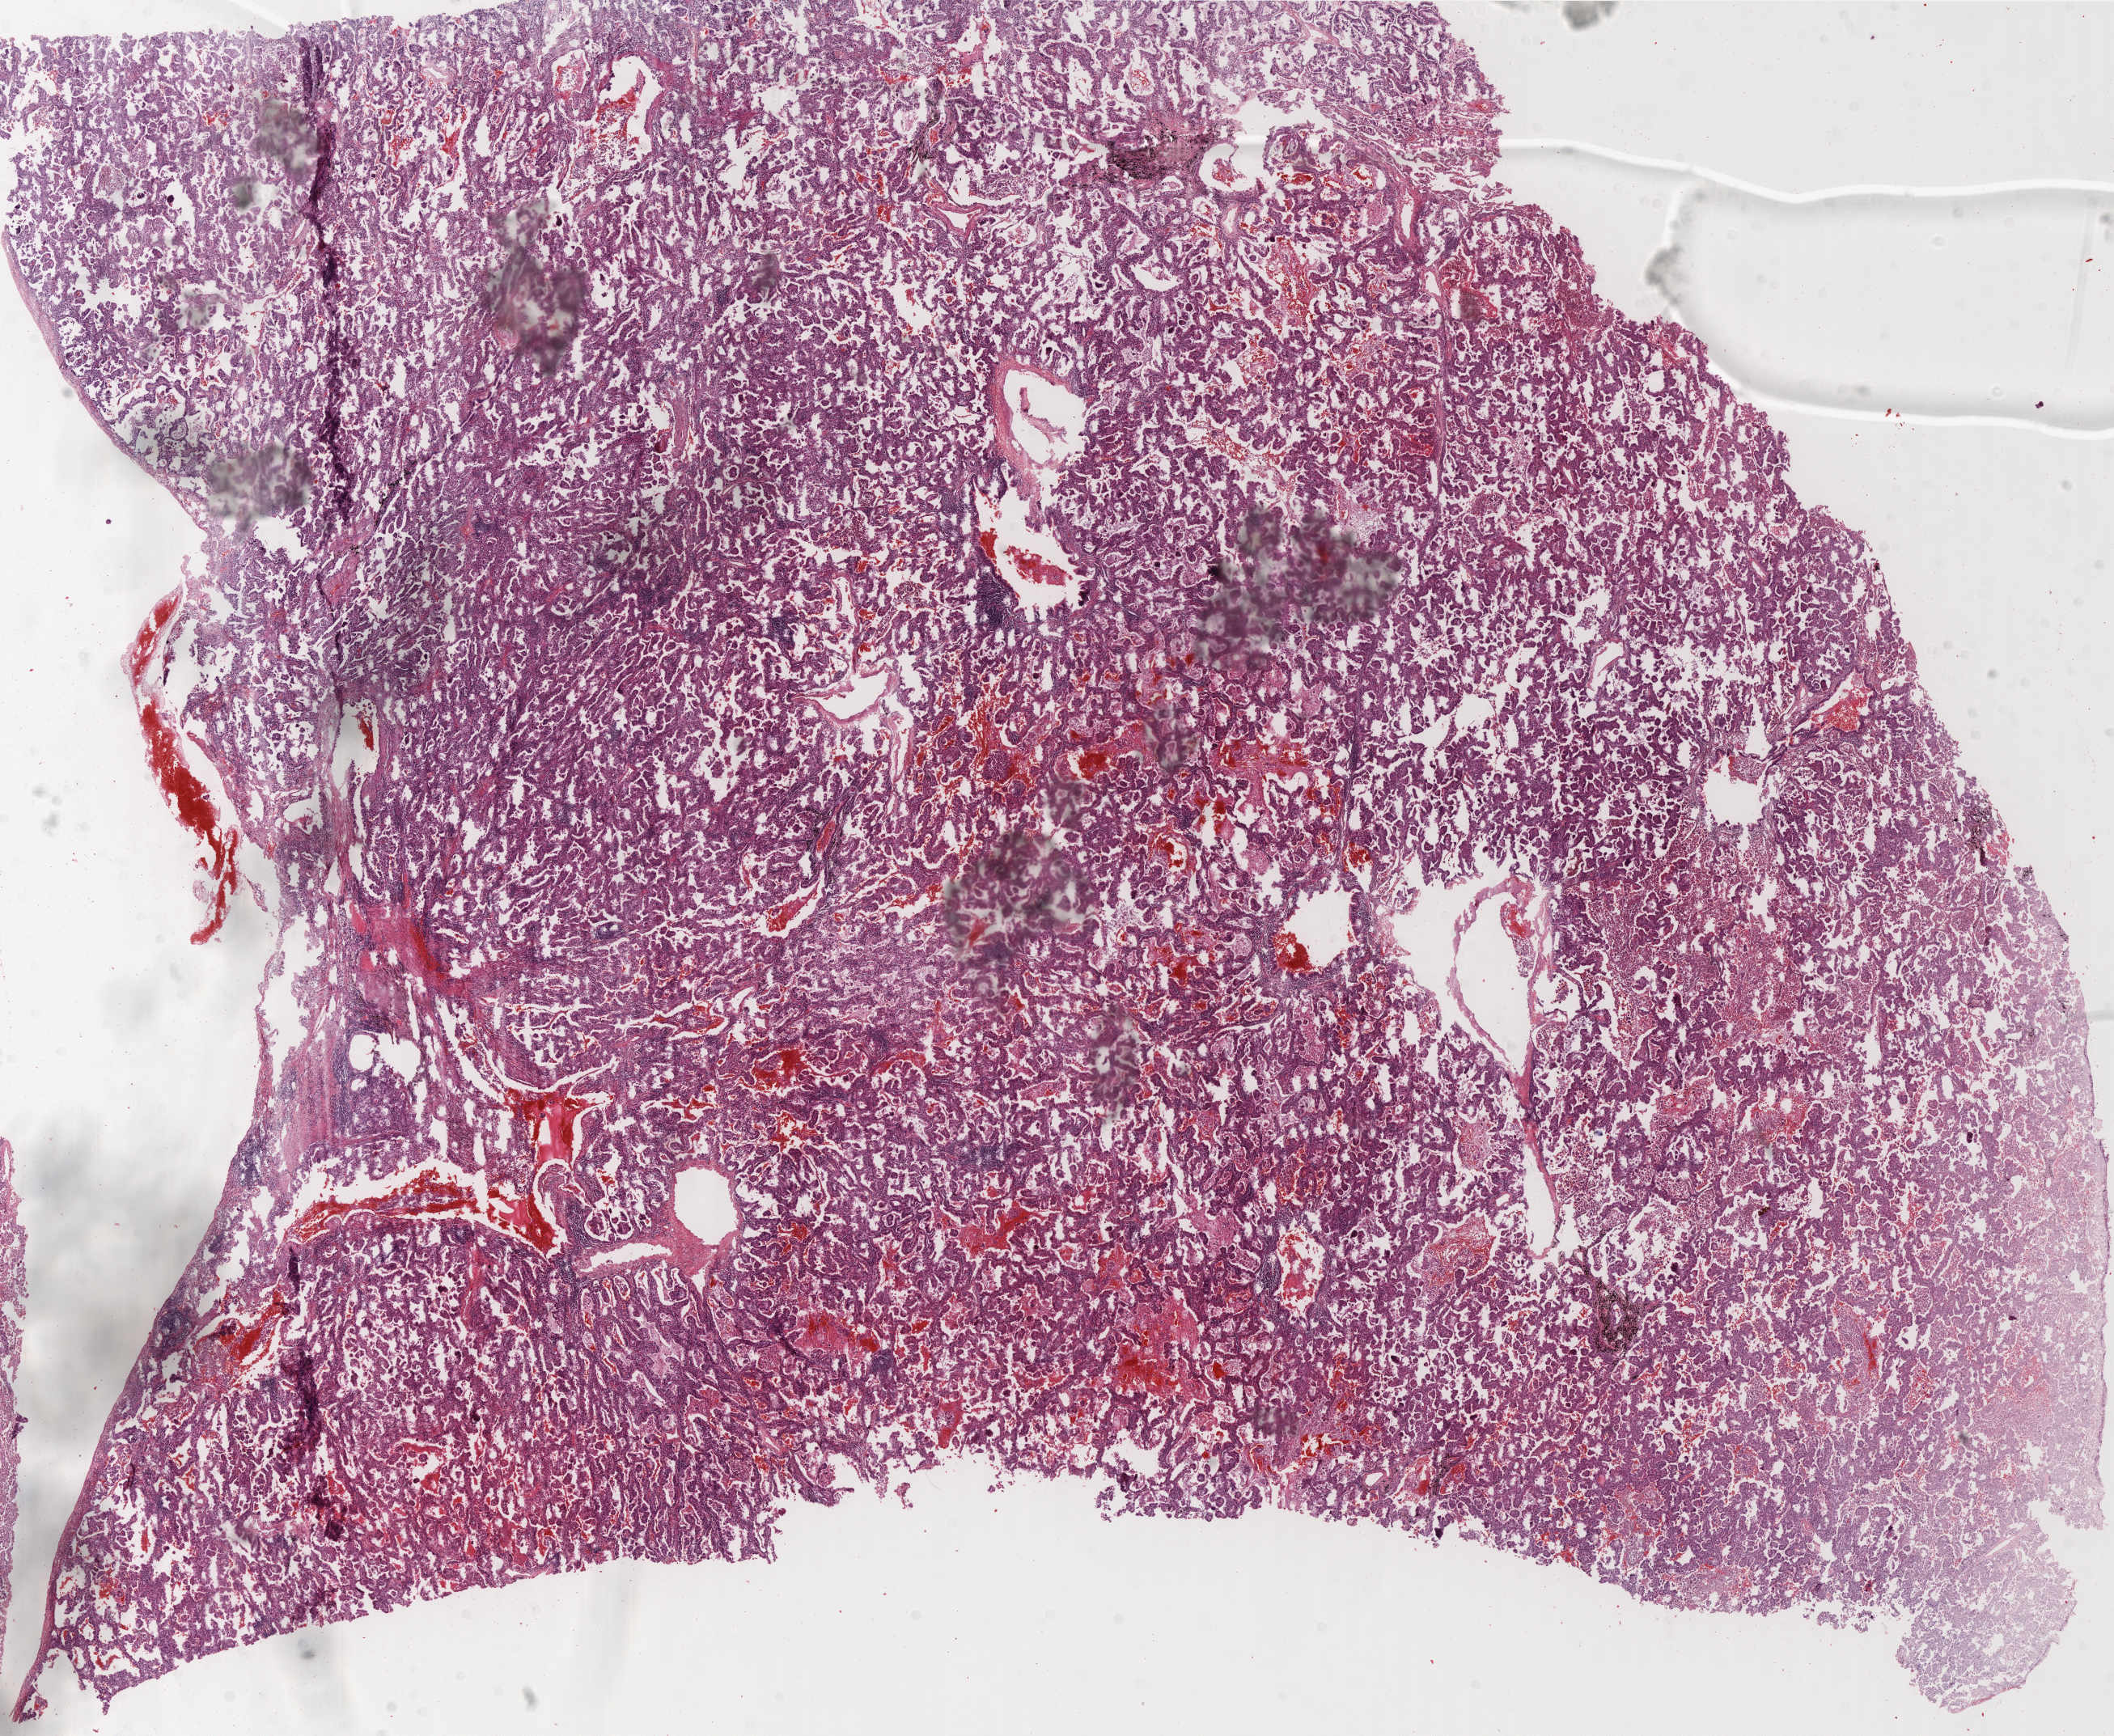
Whole-slide histology image, H&E-stained — shown as a low-resolution overview of the whole scanned area (about 21.1 x 17.3 mm, slide scanned at 40x). Formalin-fixed paraffin-embedded (FFPE) diagnostic section. Sample: primary tumour, lung. Male, age 73 years at initial diagnosis.
* pathologic diagnosis: Papillary adenocarcinoma, NOS
* AJCC pathologic stage: IB